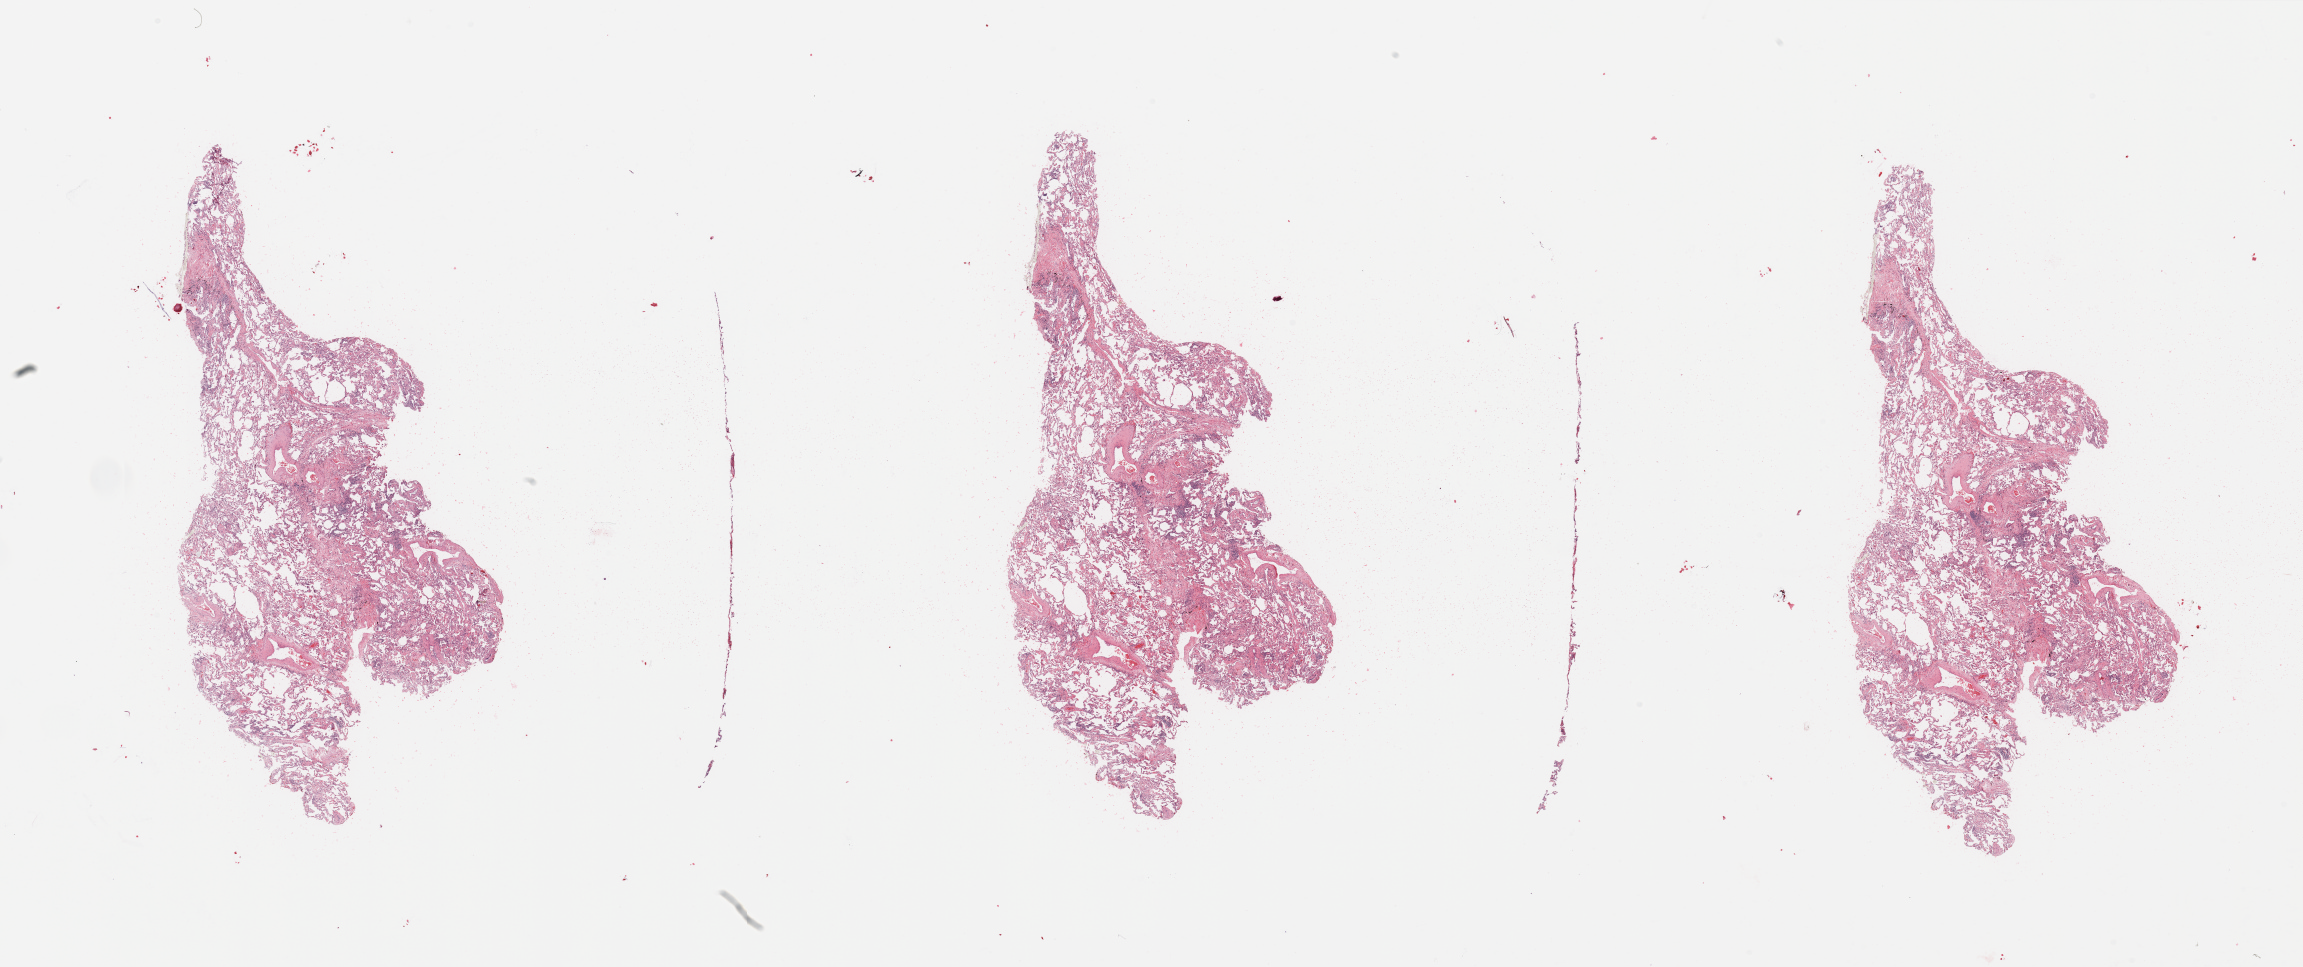
H&E whole-slide image — low-resolution overview of the scanned area, about 36.4 x 15.3 mm (from a 20x scan); normal (non-tumour) tissue sample, sampled site: lung. Female, 68 y/o.
This section: normal (non-tumour) tissue from the same patient. Patient diagnosis: Squamous cell carcinoma, NOS.